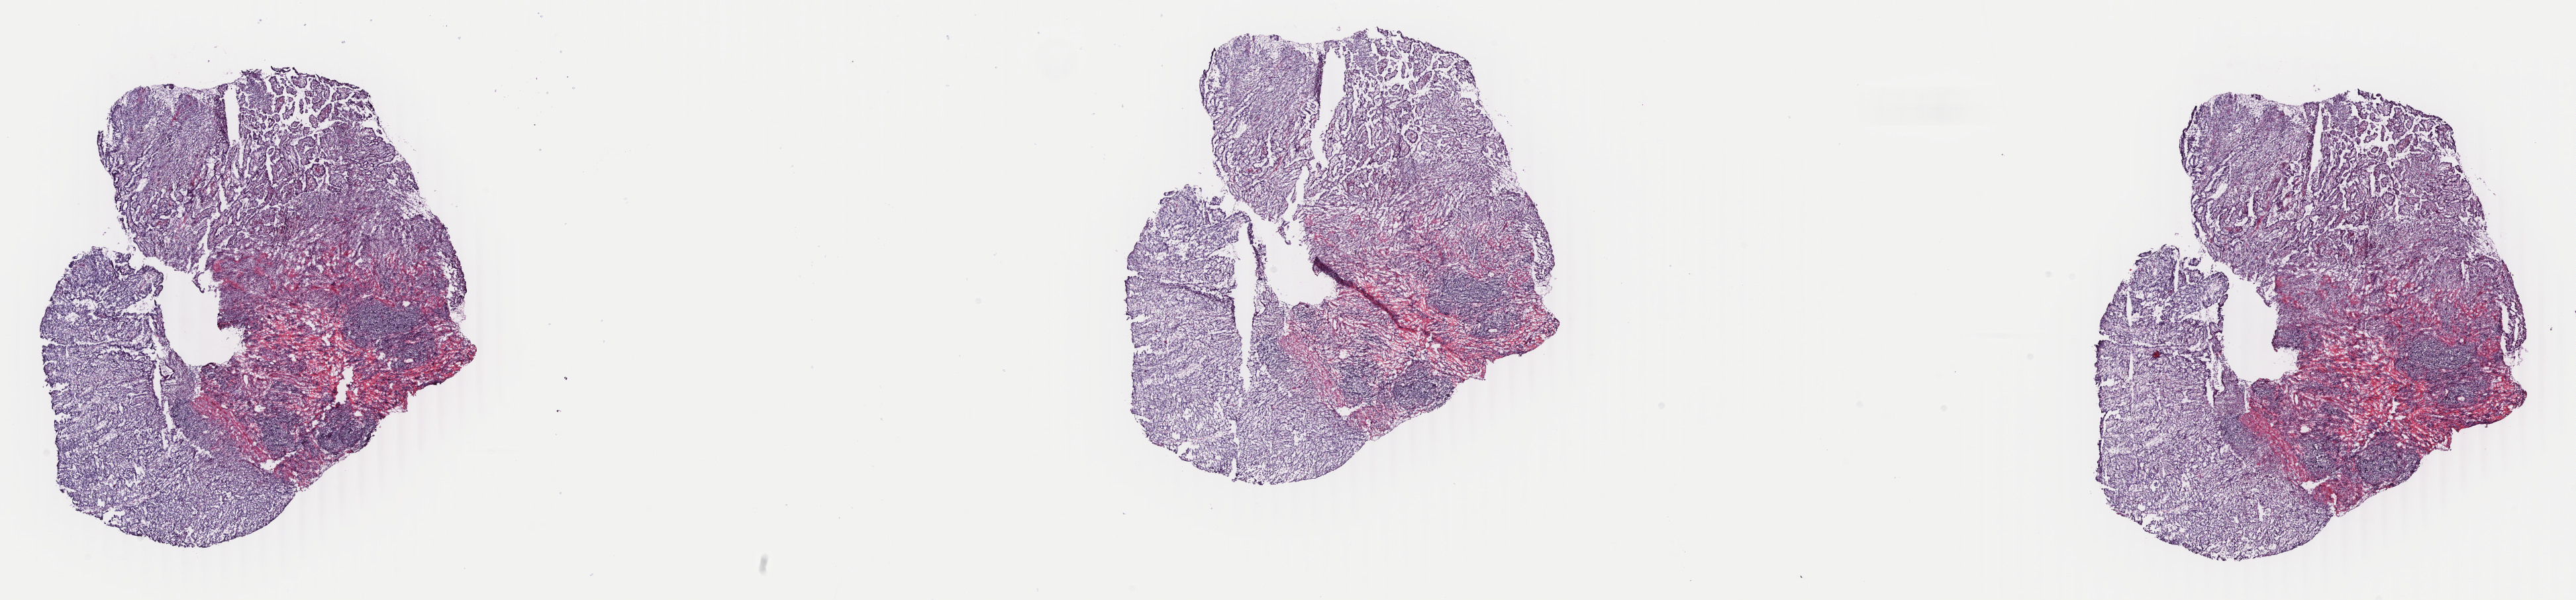
H&E whole-slide image — a low-resolution overview of the entire scanned area, about 30.9 x 7.2 mm; frozen section; sample: primary tumour, stomach. Female, age 54 years at initial diagnosis. Histologic grade: G3 (poorly differentiated). Pathologist review of this section (percent, as recorded): tumour cells 65%, tumour nuclei 65%, normal cells 0%, stromal cells 35%, necrosis 0%. Inflammatory infiltration, as recorded: lymphocyte infiltration 4%, monocyte infiltration 2%, neutrophil infiltration 6%.
AJCC pathologic stage: IB (6th edition). Histologic diagnosis: Adenocarcinoma, intestinal type (body of stomach).